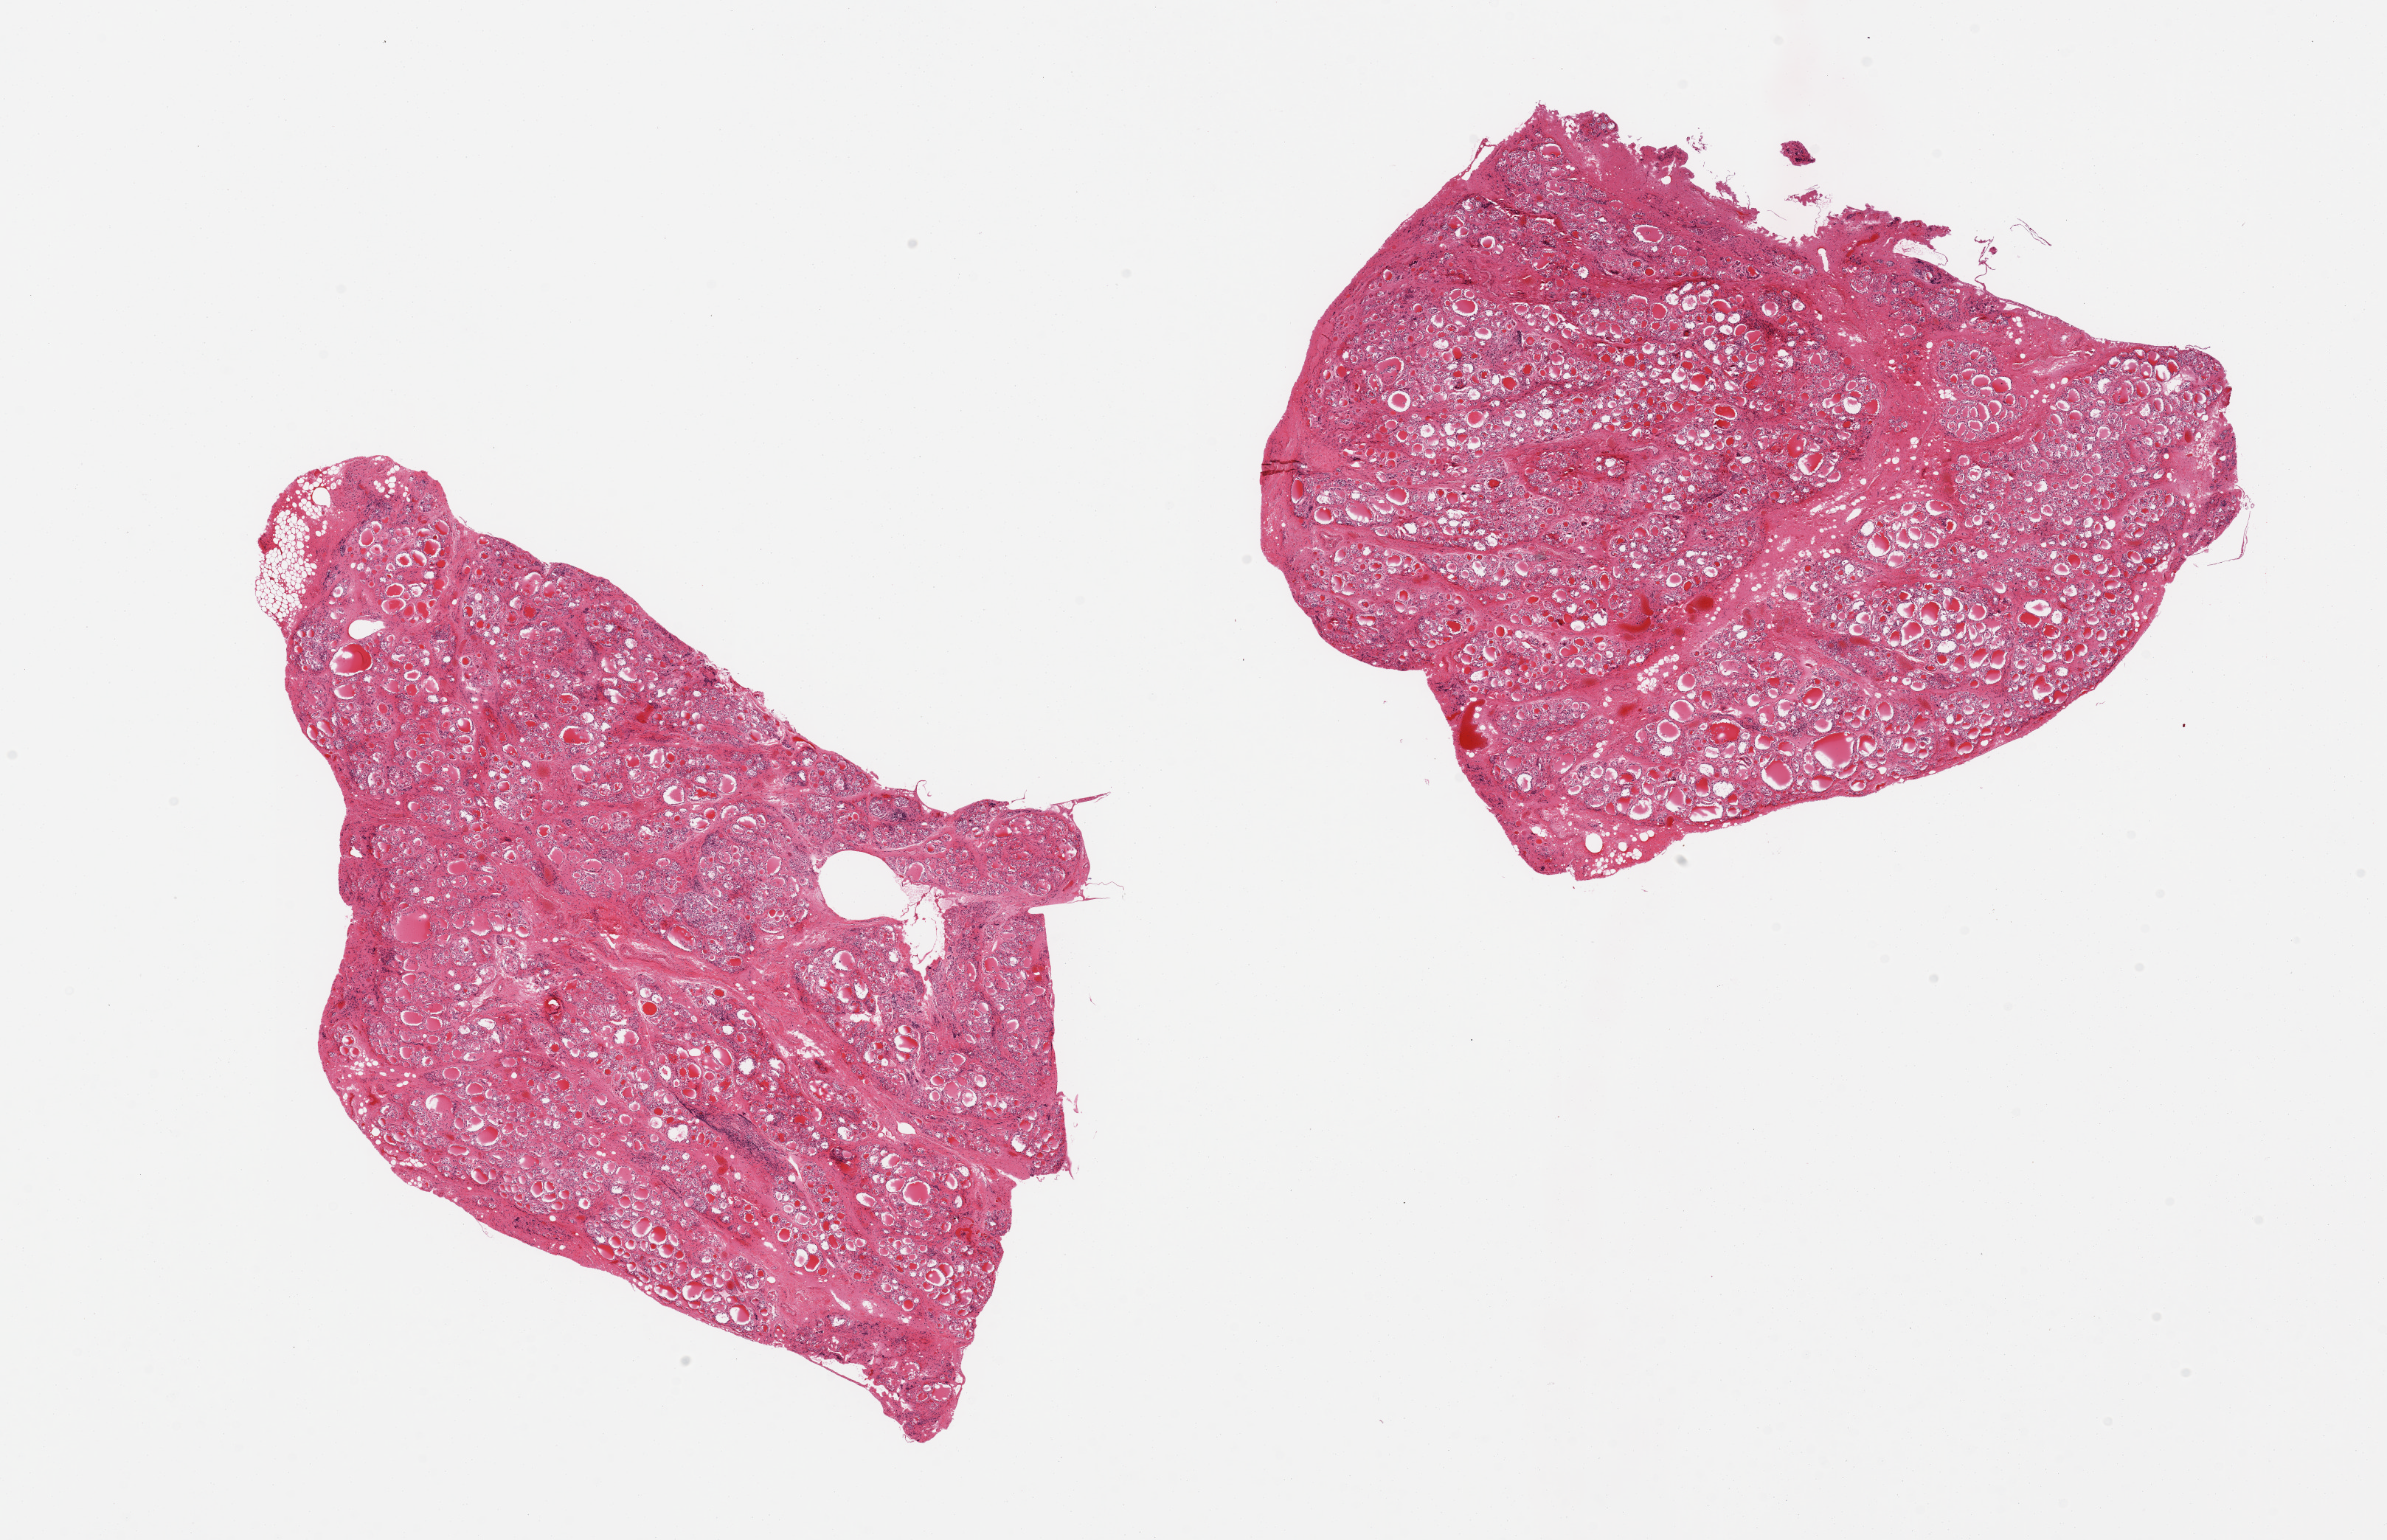
Whole-slide image, hematoxylin and eosin (H&E) stain — low-resolution overview of the scanned area, about 25.6 x 16.5 mm (slide scanned at 20x). PAXgene-fixed paraffin-embedded (PFPE) section. Section of thyroid (target tissue). Donor tissue sample. Male donor.
• reviewer comment on this tissue sample: 2 pieces, fibrosis, nodularity with few collections of lymphocytes